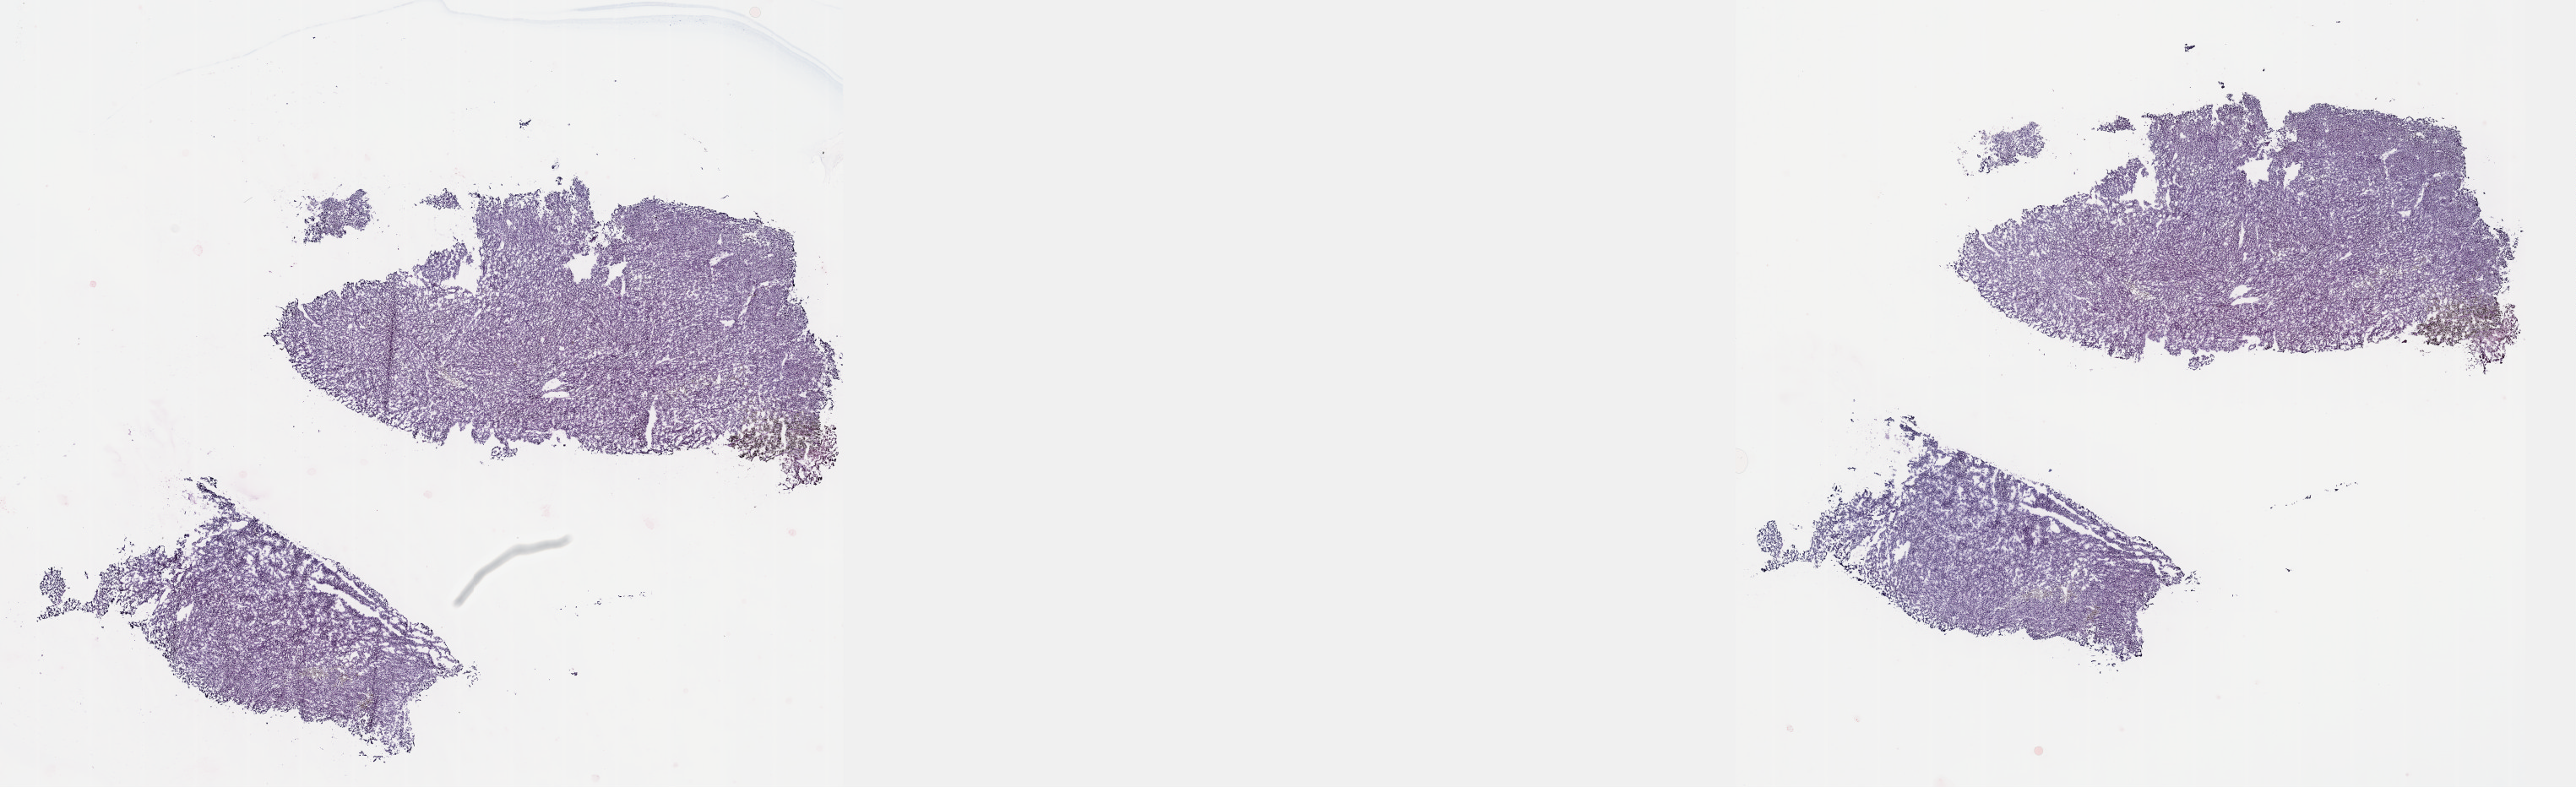
Whole-slide histology image, H&E — shown as a low-resolution overview of the whole scanned area (about 24.6 x 7.5 mm, from a 40x scan). Frozen section. Primary tumour sample from the uvea. Female, age 70 years at initial diagnosis. Composition of this section per pathologist review: tumour cells 100%, tumour nuclei 97%, normal cells 0%, stromal cells 0%, necrosis 0%. Inflammatory infiltration, as recorded: lymphocyte infiltration 0%, monocyte infiltration 0%, neutrophil infiltration 0%.
Laterality: right. Histologic diagnosis: Spindle cell melanoma, NOS (choroid). AJCC pathologic stage: IIA (7th edition).